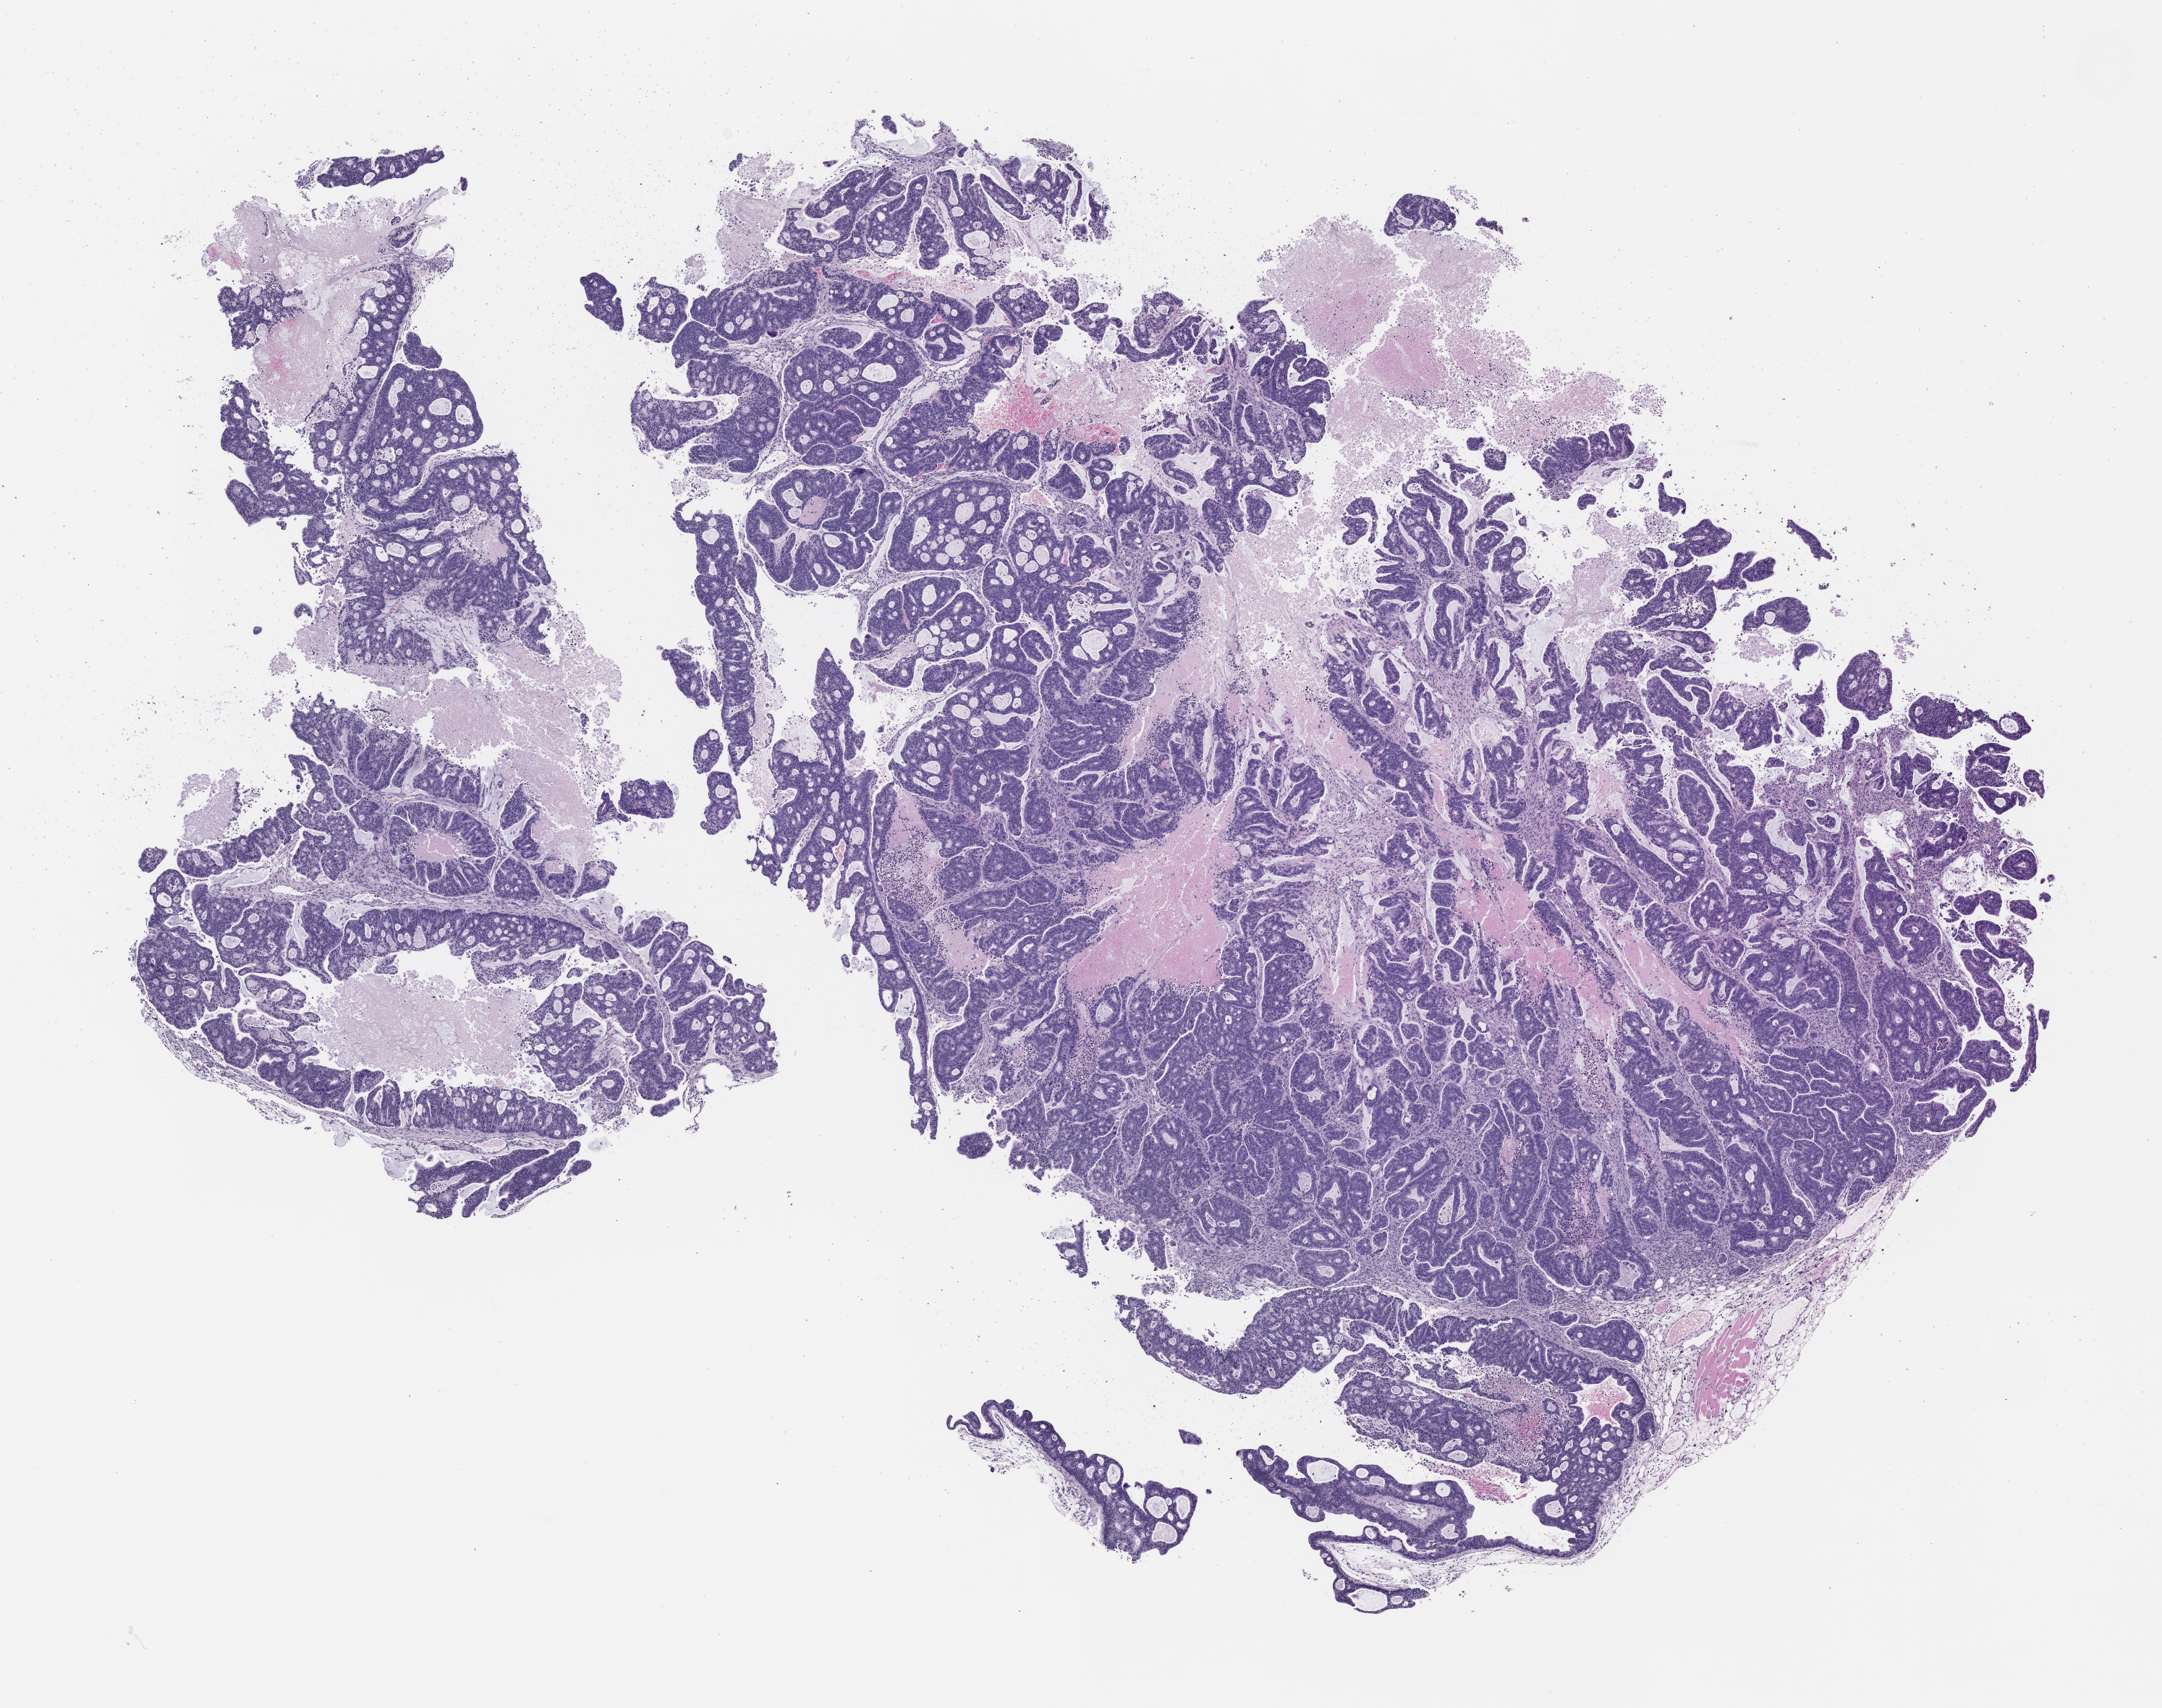
H&E whole-slide image of a patient-derived xenograft (PDX) tumor grown in a mouse, passage 1 — shown as a low-resolution overview of the whole scanned area (about 12.0 x 9.5 mm). Formalin-fixed, paraffin-embedded (FFPE) tissue. Tumor site category: colon.
Originating patient diagnosis: Colon Adenocarcinoma.